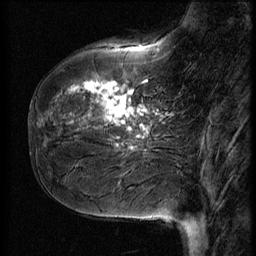
Breast MRI (dynamic contrast-enhanced), one sagittal slice; position 18 of 56 along the scan axis; 3 images stored at this slice position (order not interpretable as contrast timing); 1.5 T; TE 4.2 ms, TR 9 ms; 2.5 mm slice thickness; 256 × 256 image matrix, field of view 180 × 180 mm. Patient: female, 51 years. Case-level facts recorded for this patient, not image findings: setting: breast cancer imaged before/during neoadjuvant chemotherapy; receptor status: HR-positive, HER2-negative.
Outlined on this slice (semi-automatically segmented with operator editing):
- analysis volume of interest (the breast-tissue region the enhancement analysis was run in; not a lesion): bounding box <41,58,167,161> (left, top, right, bottom; pixels)
- tumour enhancement mask (voxels above the 140 % enhancement threshold inside the analysis volume of interest): <68,81,162,150>